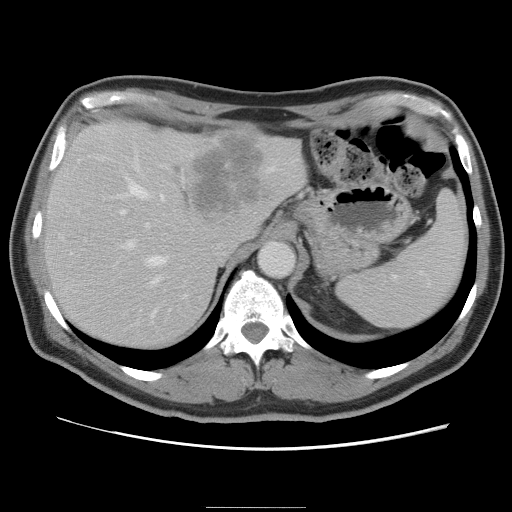
Contrast-enhanced abdominal CT, one axial slice; 120 kVp; intravenous contrast given; soft-tissue window (W 400 / L 40 HU); 5 mm slice thickness; 512 × 512 image matrix, field of view 363 × 363 mm. Male patient, age 63 years. From the clinical record (not read from this slice): diagnosis: colorectal cancer liver metastases, imaged before liver resection; multiple liver metastases: no; largest metastasis: 9 cm; disease in both lobes: no.
Annotated regions visible in this slice (expert manual segmentation):
- hepatic veins: box from (x=99, y=159) to (x=169, y=318) px
- liver: (x=43, y=120)–(x=307, y=349)
- planned liver remnant (the part of the liver to remain after resection): (x=43, y=154)–(x=218, y=349)
- portal vein (with intrahepatic branches): (x=118, y=209)–(x=188, y=298)
- liver metastasis: (x=194, y=136)–(x=263, y=213)